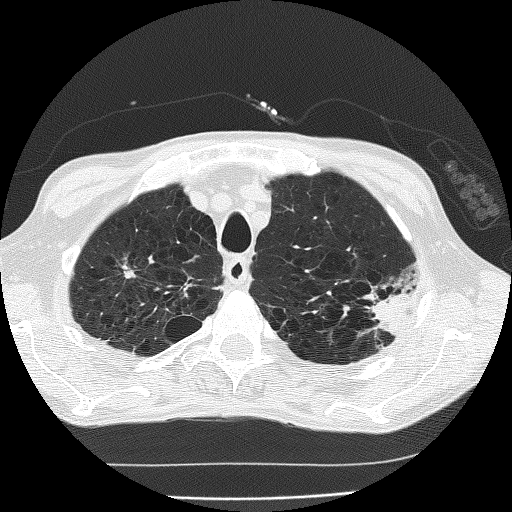
Low-dose screening chest CT, one axial slice. Position 154 of 185 along the scan axis. Reconstruction kernel FC51. Lung window (W 1500 / L -600 HU). 512 × 512 image matrix, field of view 320 × 320 mm.
Annotated regions visible in this slice (expert manual segmentation):
- lesion 1 (tumor, upper lobe of left lung): bounding box [x1, y1, x2, y2] px = [369, 294, 413, 333]